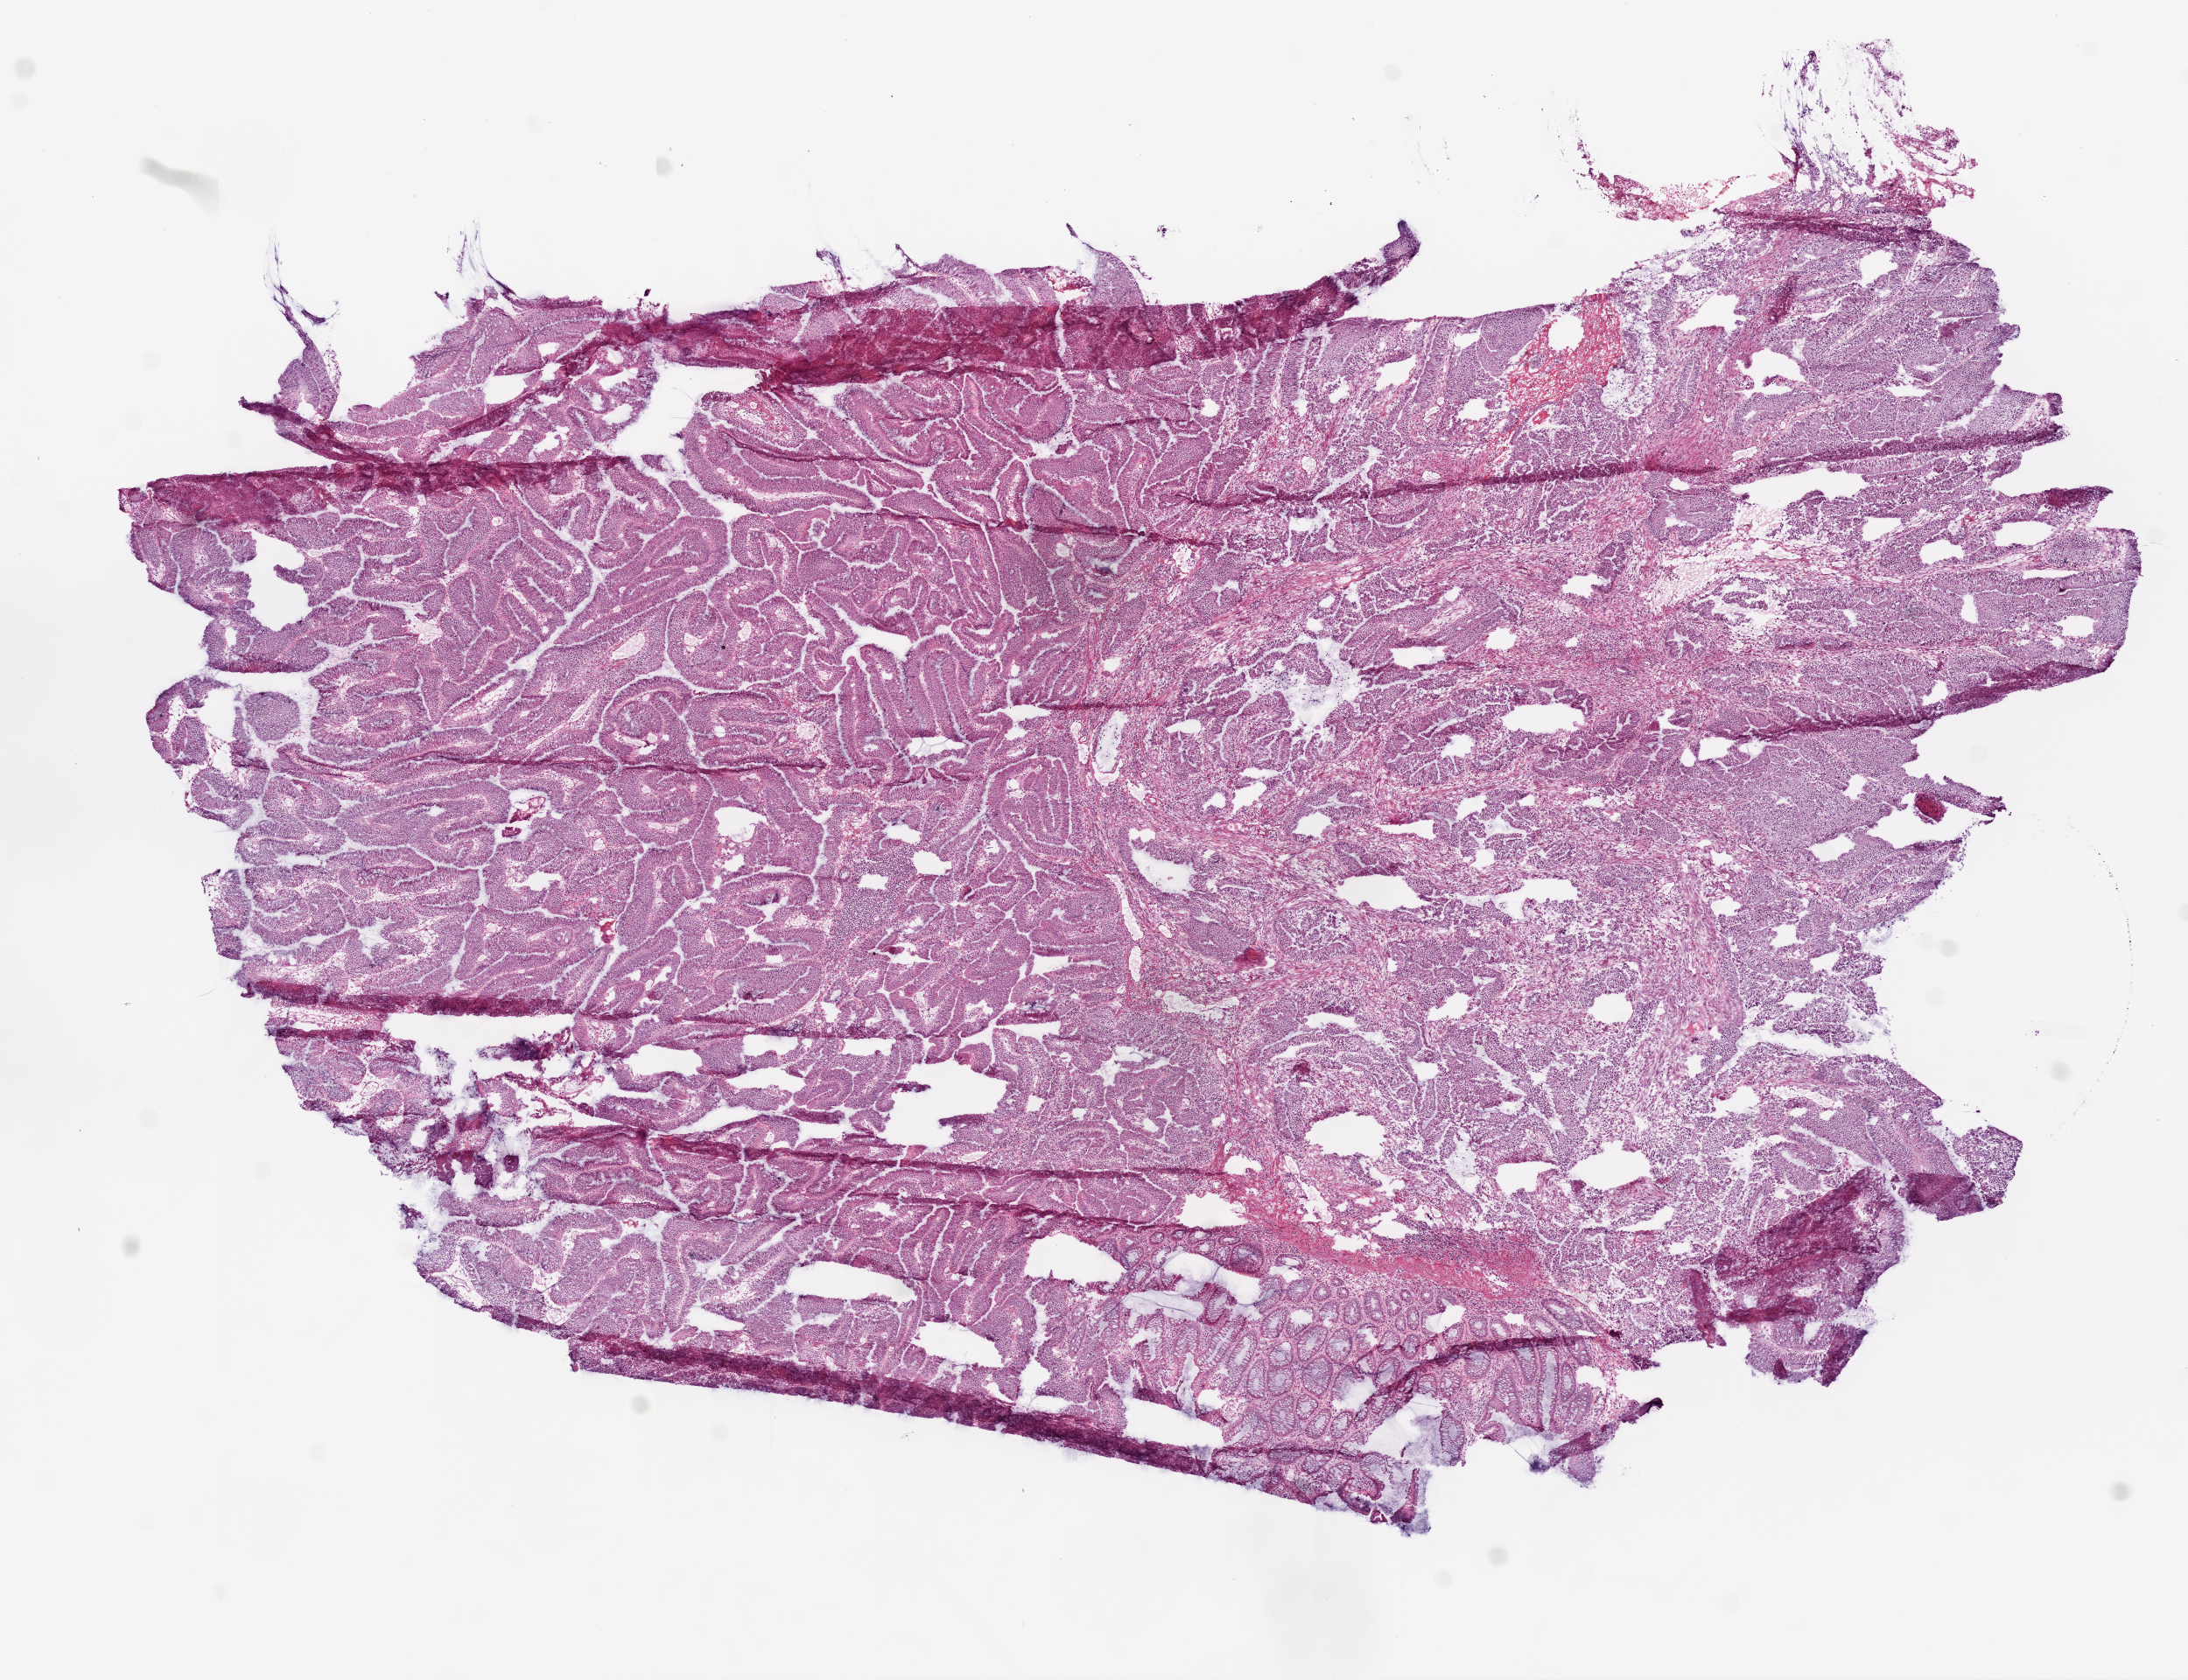
Hematoxylin and eosin (H&E) stained whole-slide image, a low-resolution overview of the entire scanned area, about 10.0 x 7.7 mm, frozen section from the bottom of the tissue portion, primary tumour sample from the colon. Female, age 71 years at initial diagnosis. Slide review estimates, as recorded: tumour cells 87%, tumour nuclei 85%, normal cells 5%, stromal cells 8%, necrosis 0%.
AJCC pathologic stage: I (6th edition). Histologic diagnosis: Mucinous adenocarcinoma. Lymph nodes positive (case pathology): 0 of 12 examined. TNM: T2 N0 M0.